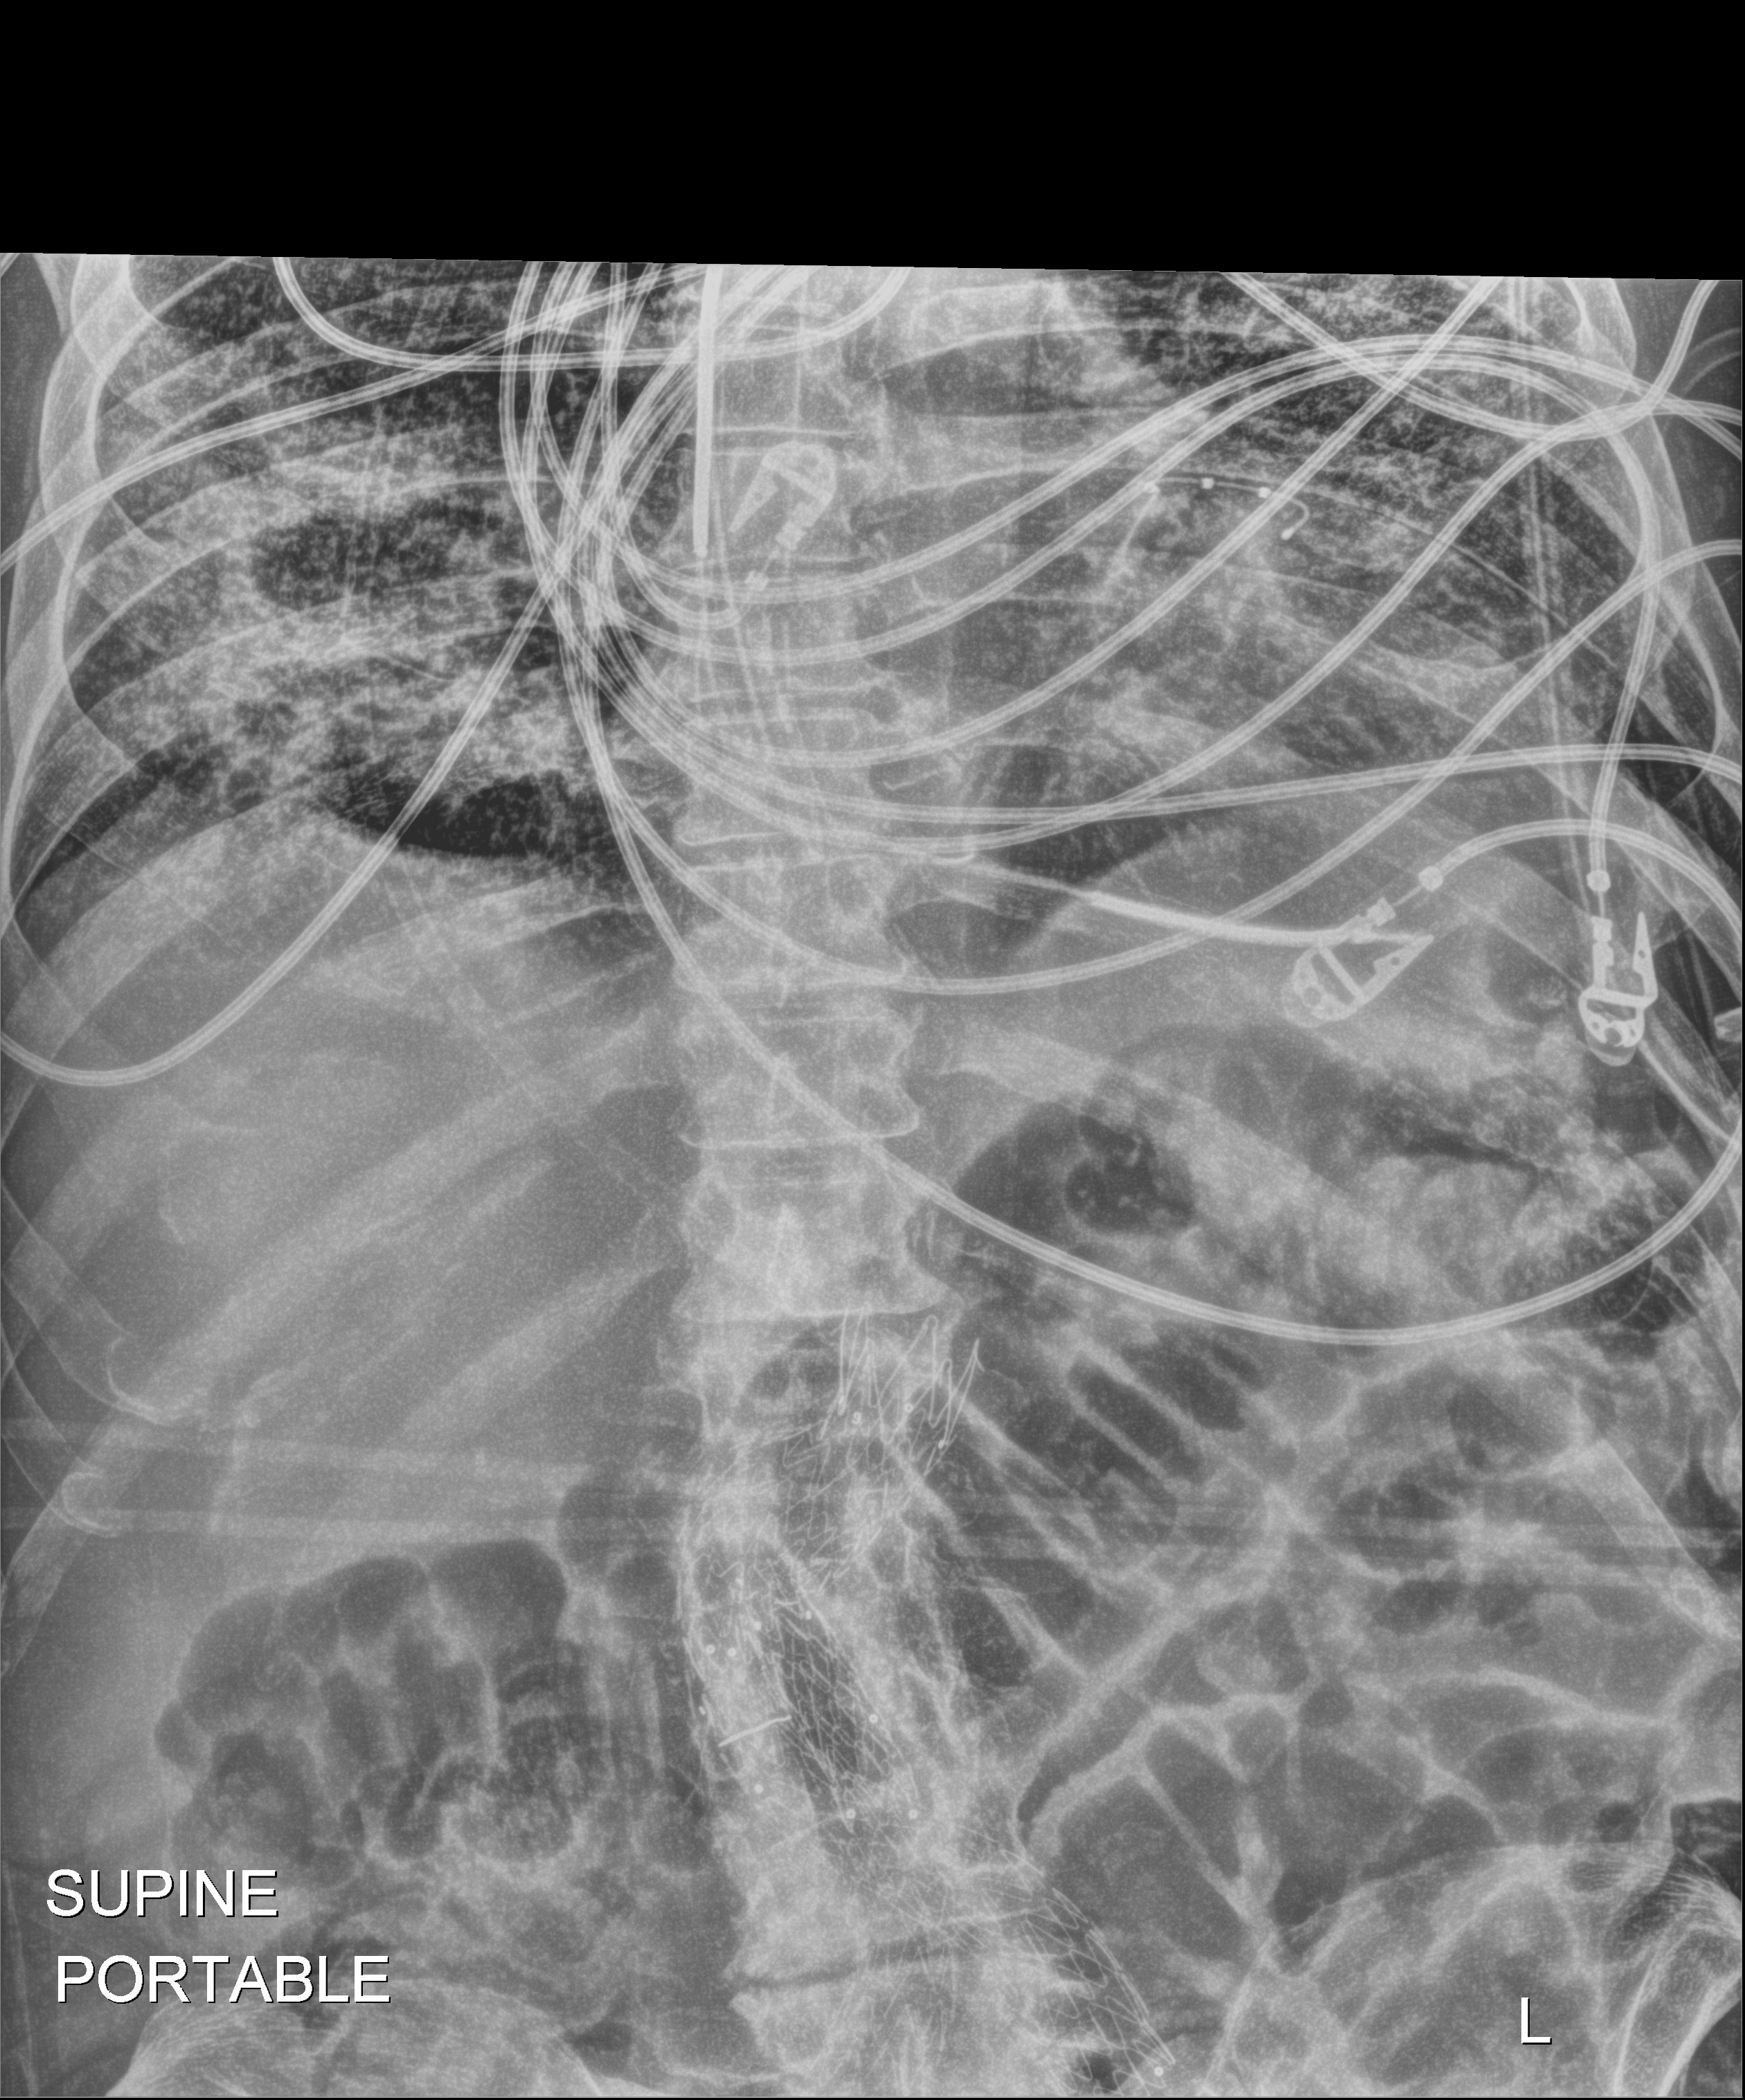
Bedside abdomen radiograph (digital radiography); anteroposterior (AP) projection. Male patient hospitalised with COVID-19, age 60–74 years.
Hospital-stay facts (about this admission, not read from this image; timing relative to this image not recorded):
- admitted to intensive care during this hospital stay: yes
- other chronic lung disease (admission record): no
- hypertension (admission record): yes